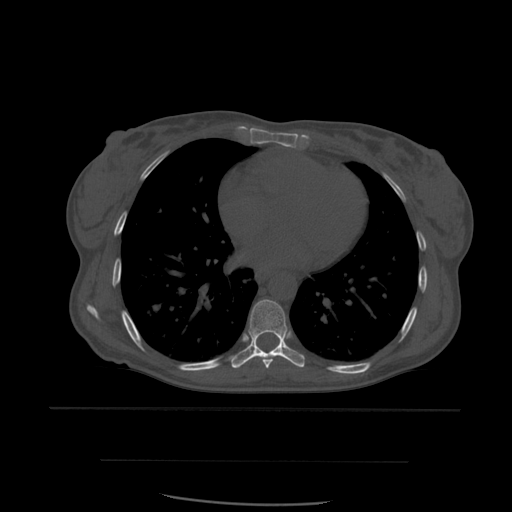
CT including the spine, one axial slice; position 360 of 574 along the scan axis; bone window (W 1800 / L 400 HU); 512 × 512 image matrix, field of view 392 × 392 mm. Patient age 48 years. Case-level facts recorded for this patient, not image findings: primary cancer: lung; vertebrae with lytic lesions (as recorded): T11.
Annotated regions visible in this slice (semi-automatically segmented with operator editing):
- T6 vertebra: bounding box <249,332,253,340> (left, top, right, bottom; pixels)
- T7 vertebra: <262,359,273,369>
- T8 vertebra: <231,300,305,369>